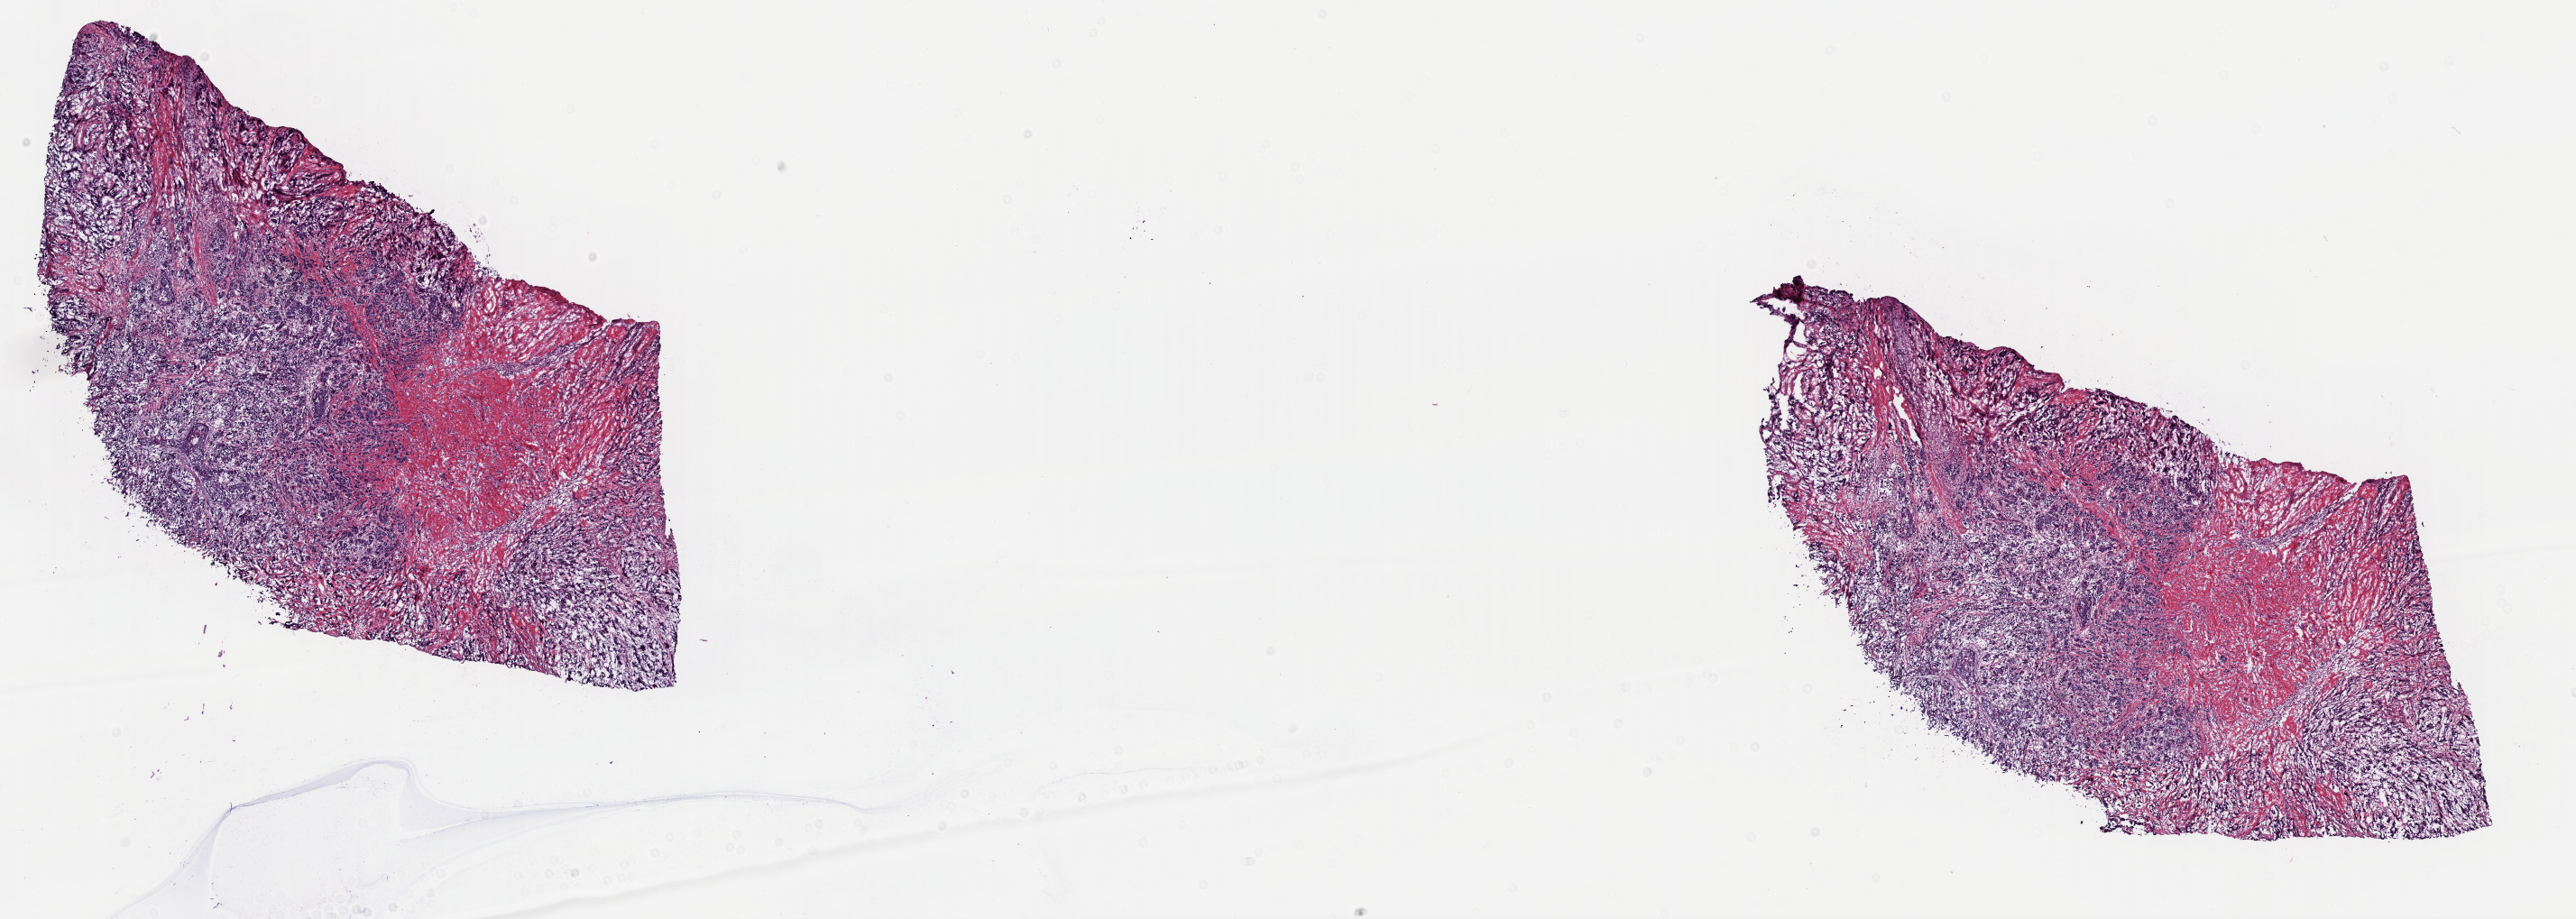
H&E whole-slide image — low-resolution overview of the scanned area, about 22.6 x 8.0 mm (from a 40x scan), frozen section, breast, primary tumour sample. Female patient; age at initial diagnosis 58 years. Pathologist review of this section (percent, as recorded): tumour cells 70%, tumour nuclei 85%, normal cells 0%, stromal cells 28%, necrosis 2%. Inflammatory infiltration, as recorded: lymphocyte infiltration 1%, monocyte infiltration 0%, neutrophil infiltration 0%.
TNM: T2 N0 M0. Lymph nodes positive (case pathology): 0 of 4 examined. Histologic diagnosis: Infiltrating duct carcinoma, NOS. AJCC pathologic stage: IIA (6th edition).